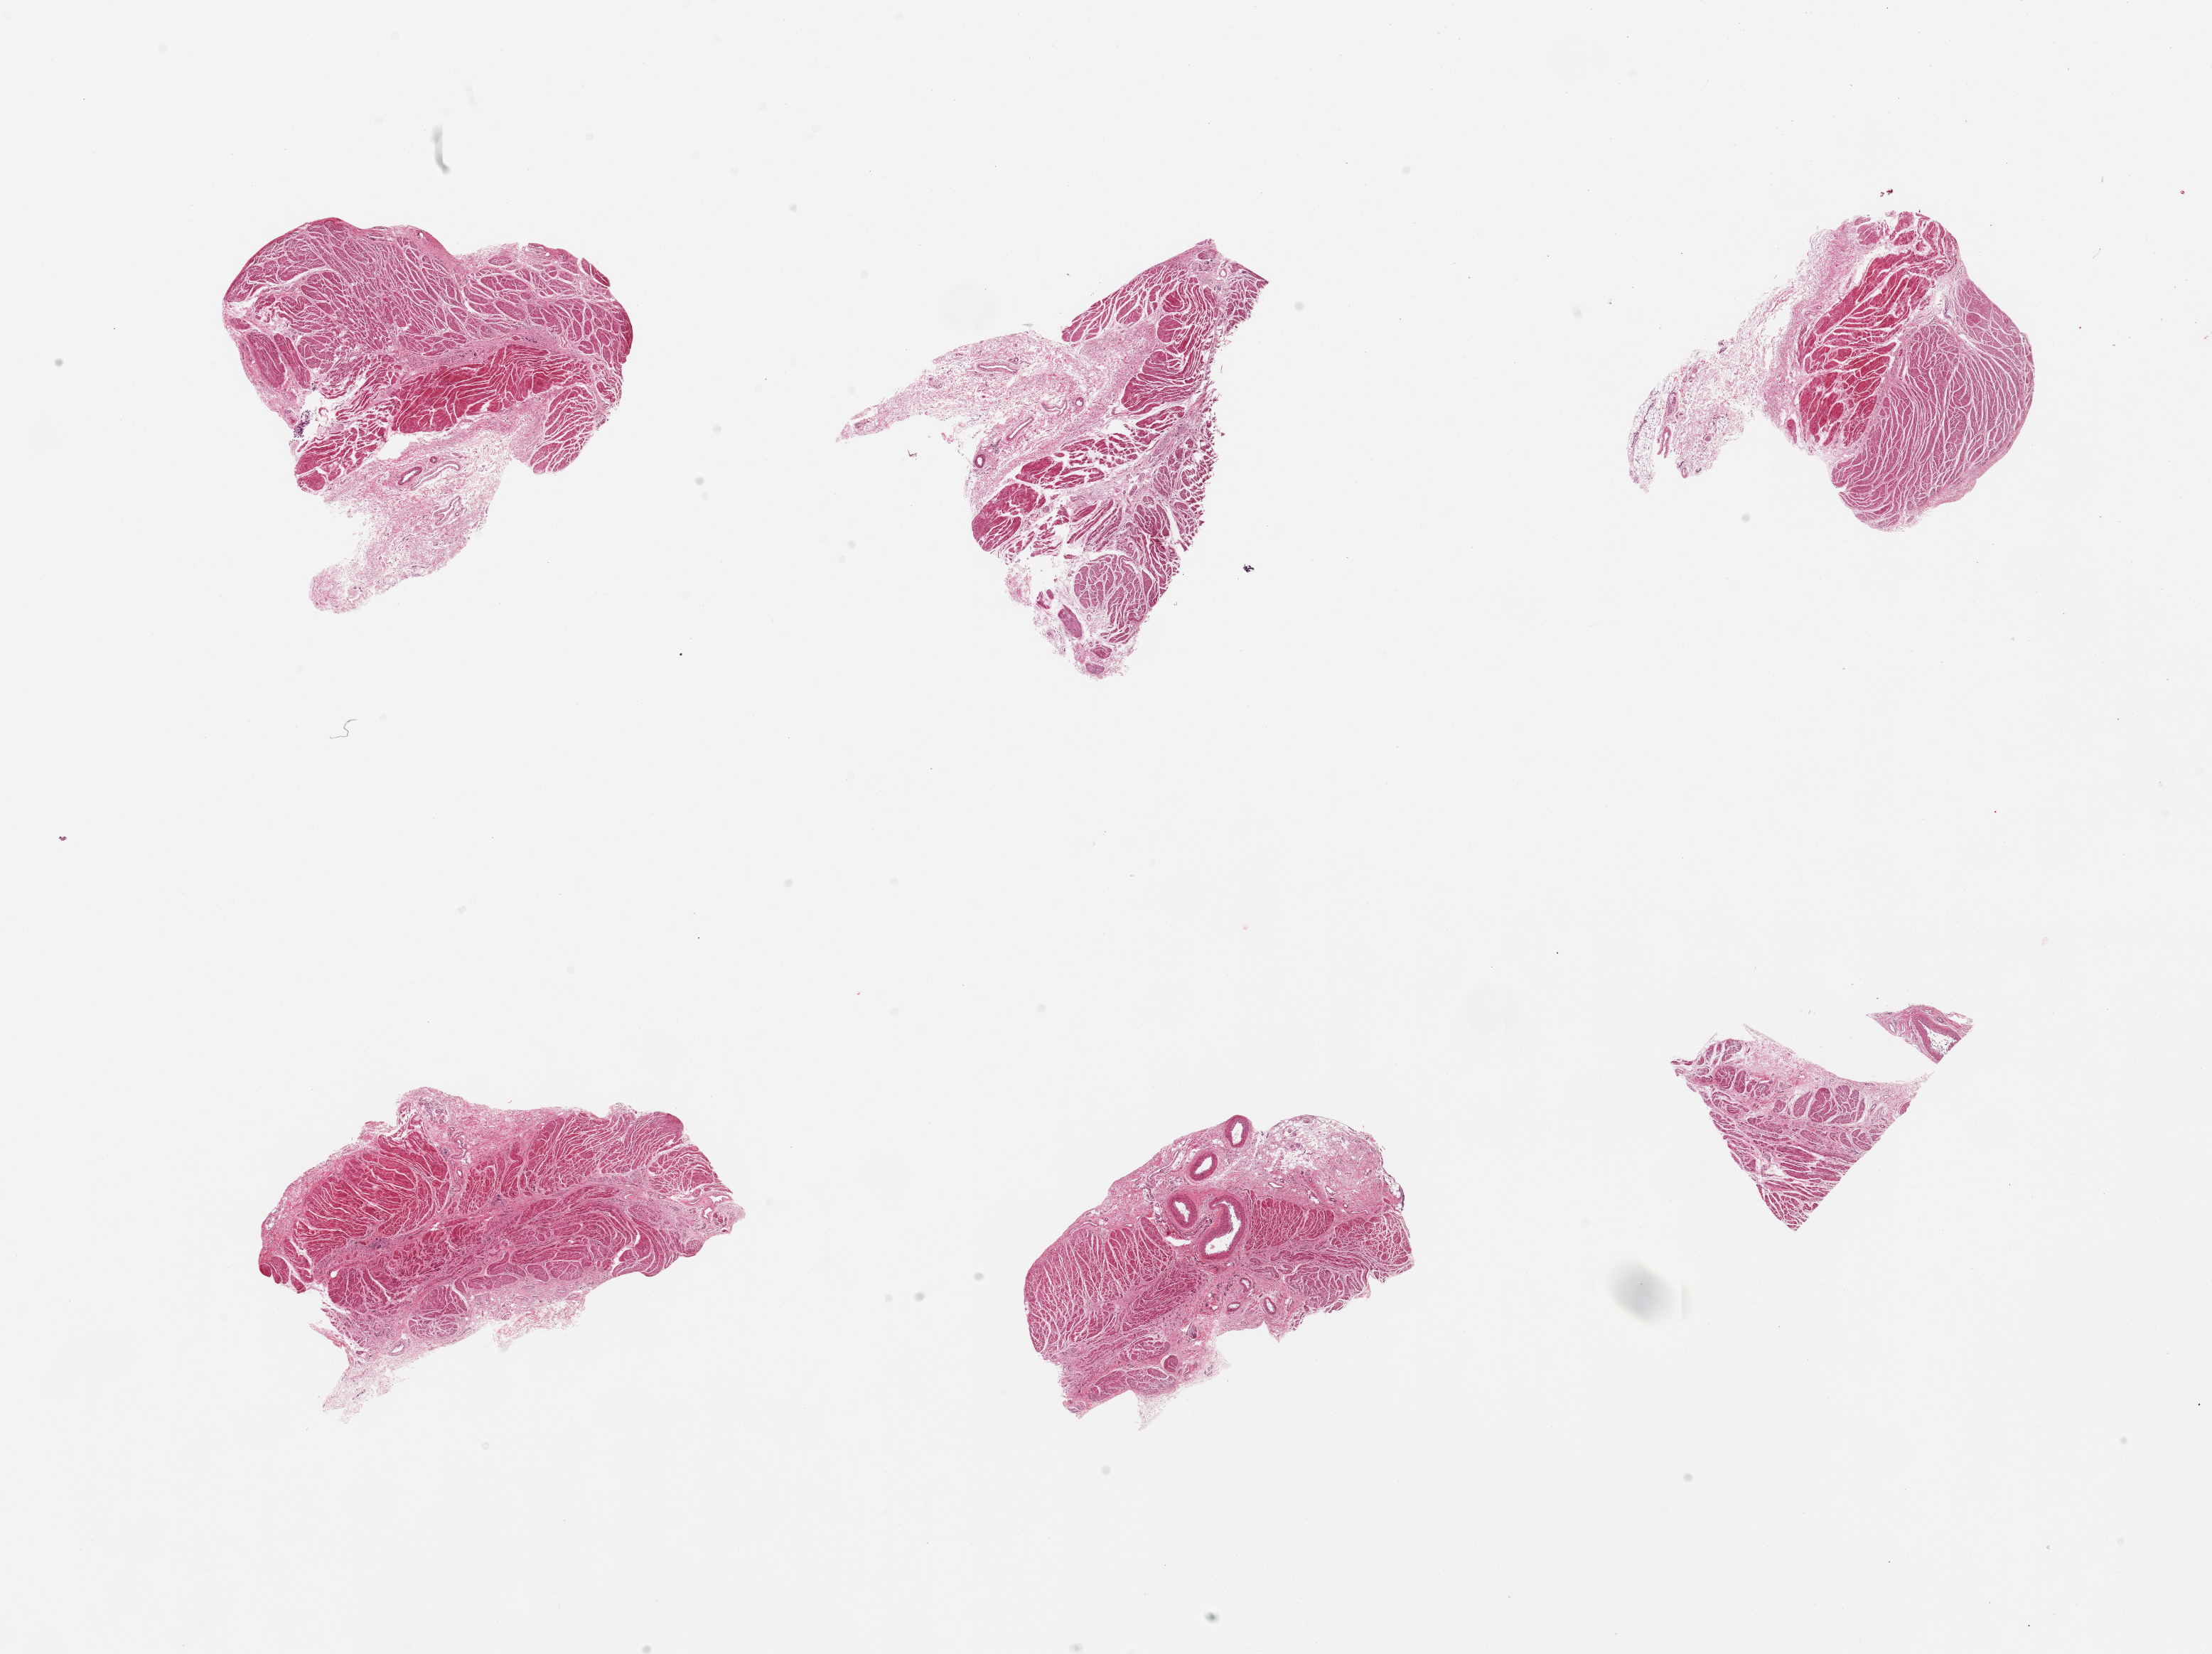
Digitized hematoxylin and eosin (H&E)-stained section, brightfield, low-resolution overview of the scanned area, about 24.6 x 18.4 mm. PAXgene-fixed, paraffin-embedded tissue. Sampled site (target tissue): gastroesophageal junction. Donor tissue sample.
Review note (as recorded): 6 pieces; up to 40% perimuscular stroma.